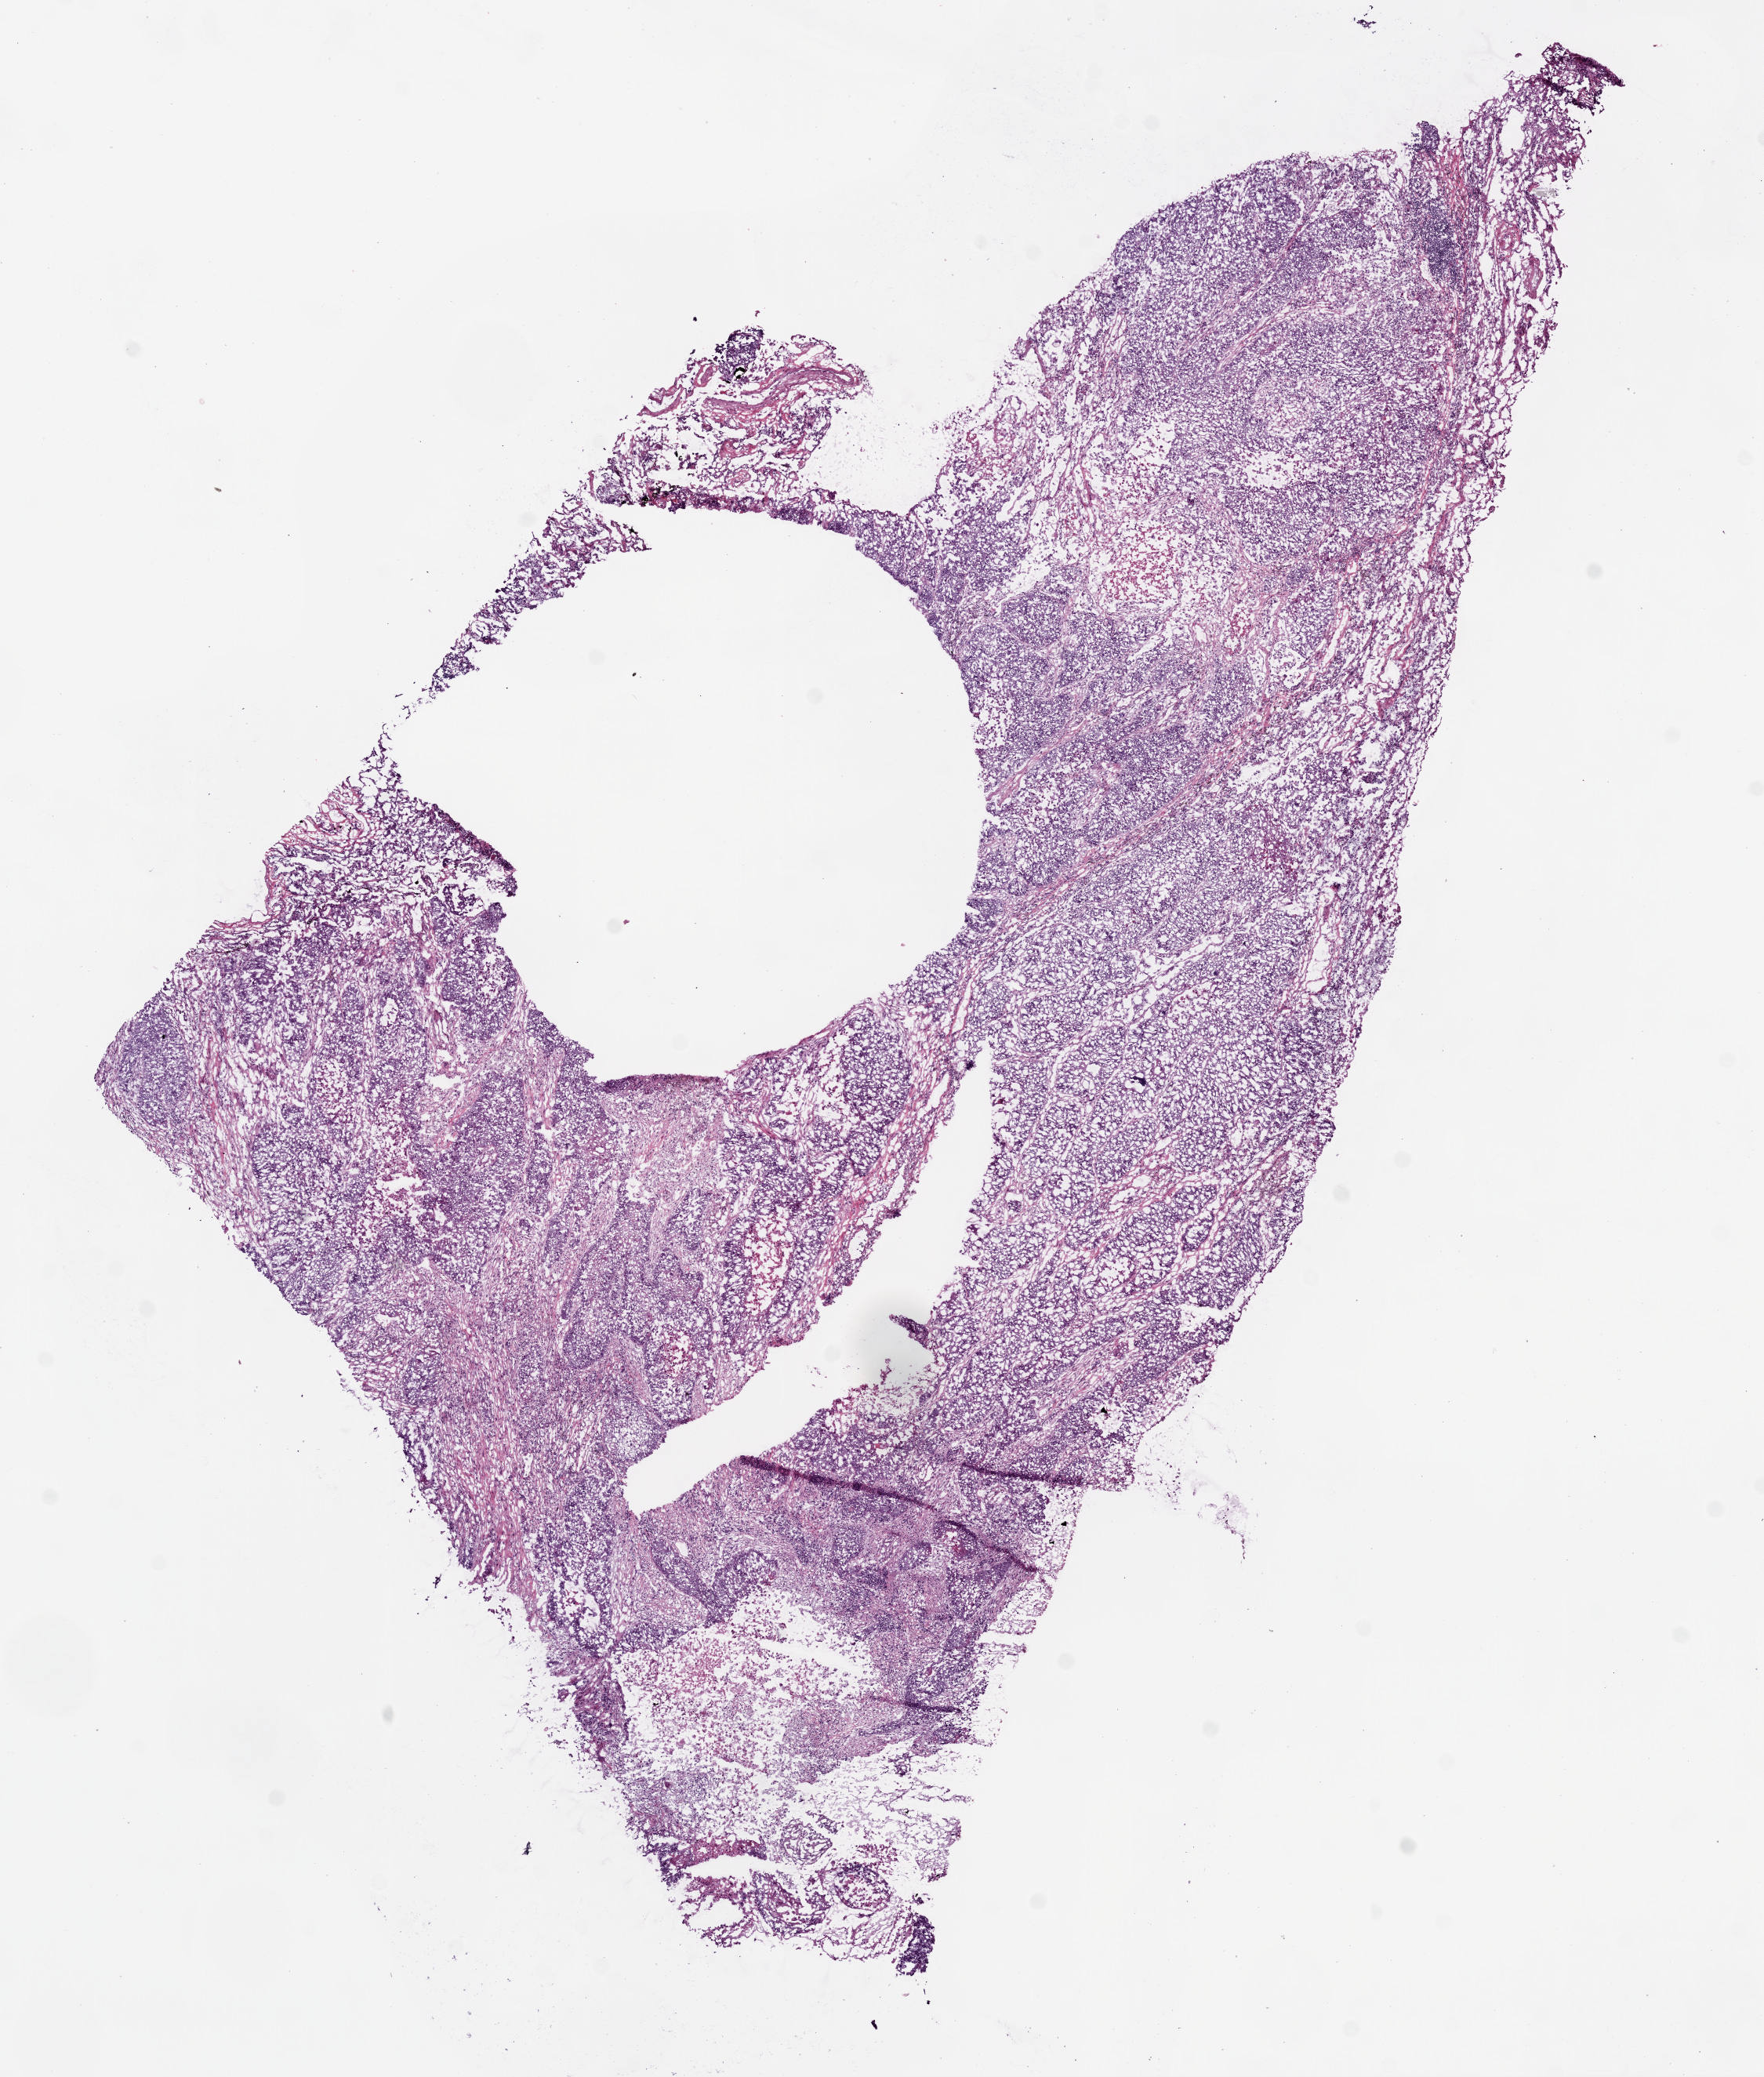
Whole-slide histology image, H&E — shown as a low-resolution overview of the whole scanned area (about 9.0 x 10.6 mm, acquisition: 20x scan); frozen section from the bottom of the tissue portion; primary tumour sample from the lung. Male patient; age at initial diagnosis 55 years. Slide review estimates, as recorded: tumour cells 80%, tumour nuclei 70%, normal cells 0%, stromal cells 15%, necrosis 5%.
AJCC pathologic stage: IA (5th edition). Laterality: left. Diagnosis: Squamous cell carcinoma, NOS (lower lobe, lung).